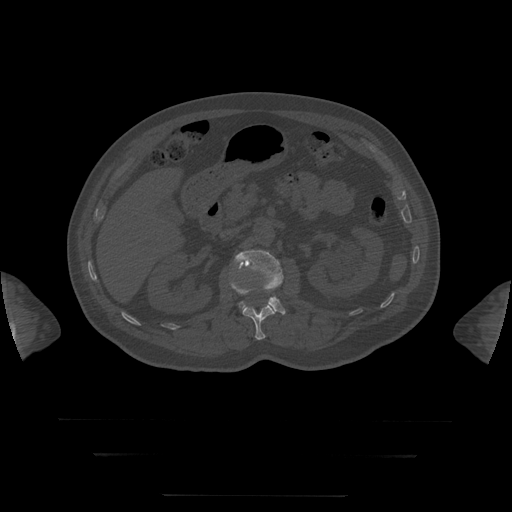
CT including the spine, one axial slice. Slice 37 of 397 in the series (ordered by position). 120 kVp. Bone window (W 1800 / L 400 HU). 1.25 mm slice thickness. 512 × 512 image matrix, field of view 510 × 510 mm. Patient age 73 years. Case-level facts recorded for this patient, not image findings: primary cancer: prostate.
Structures marked on this image (semi-automatically segmented with operator editing):
- L1 vertebra: bounding box <230,279,275,340> (left, top, right, bottom; pixels)